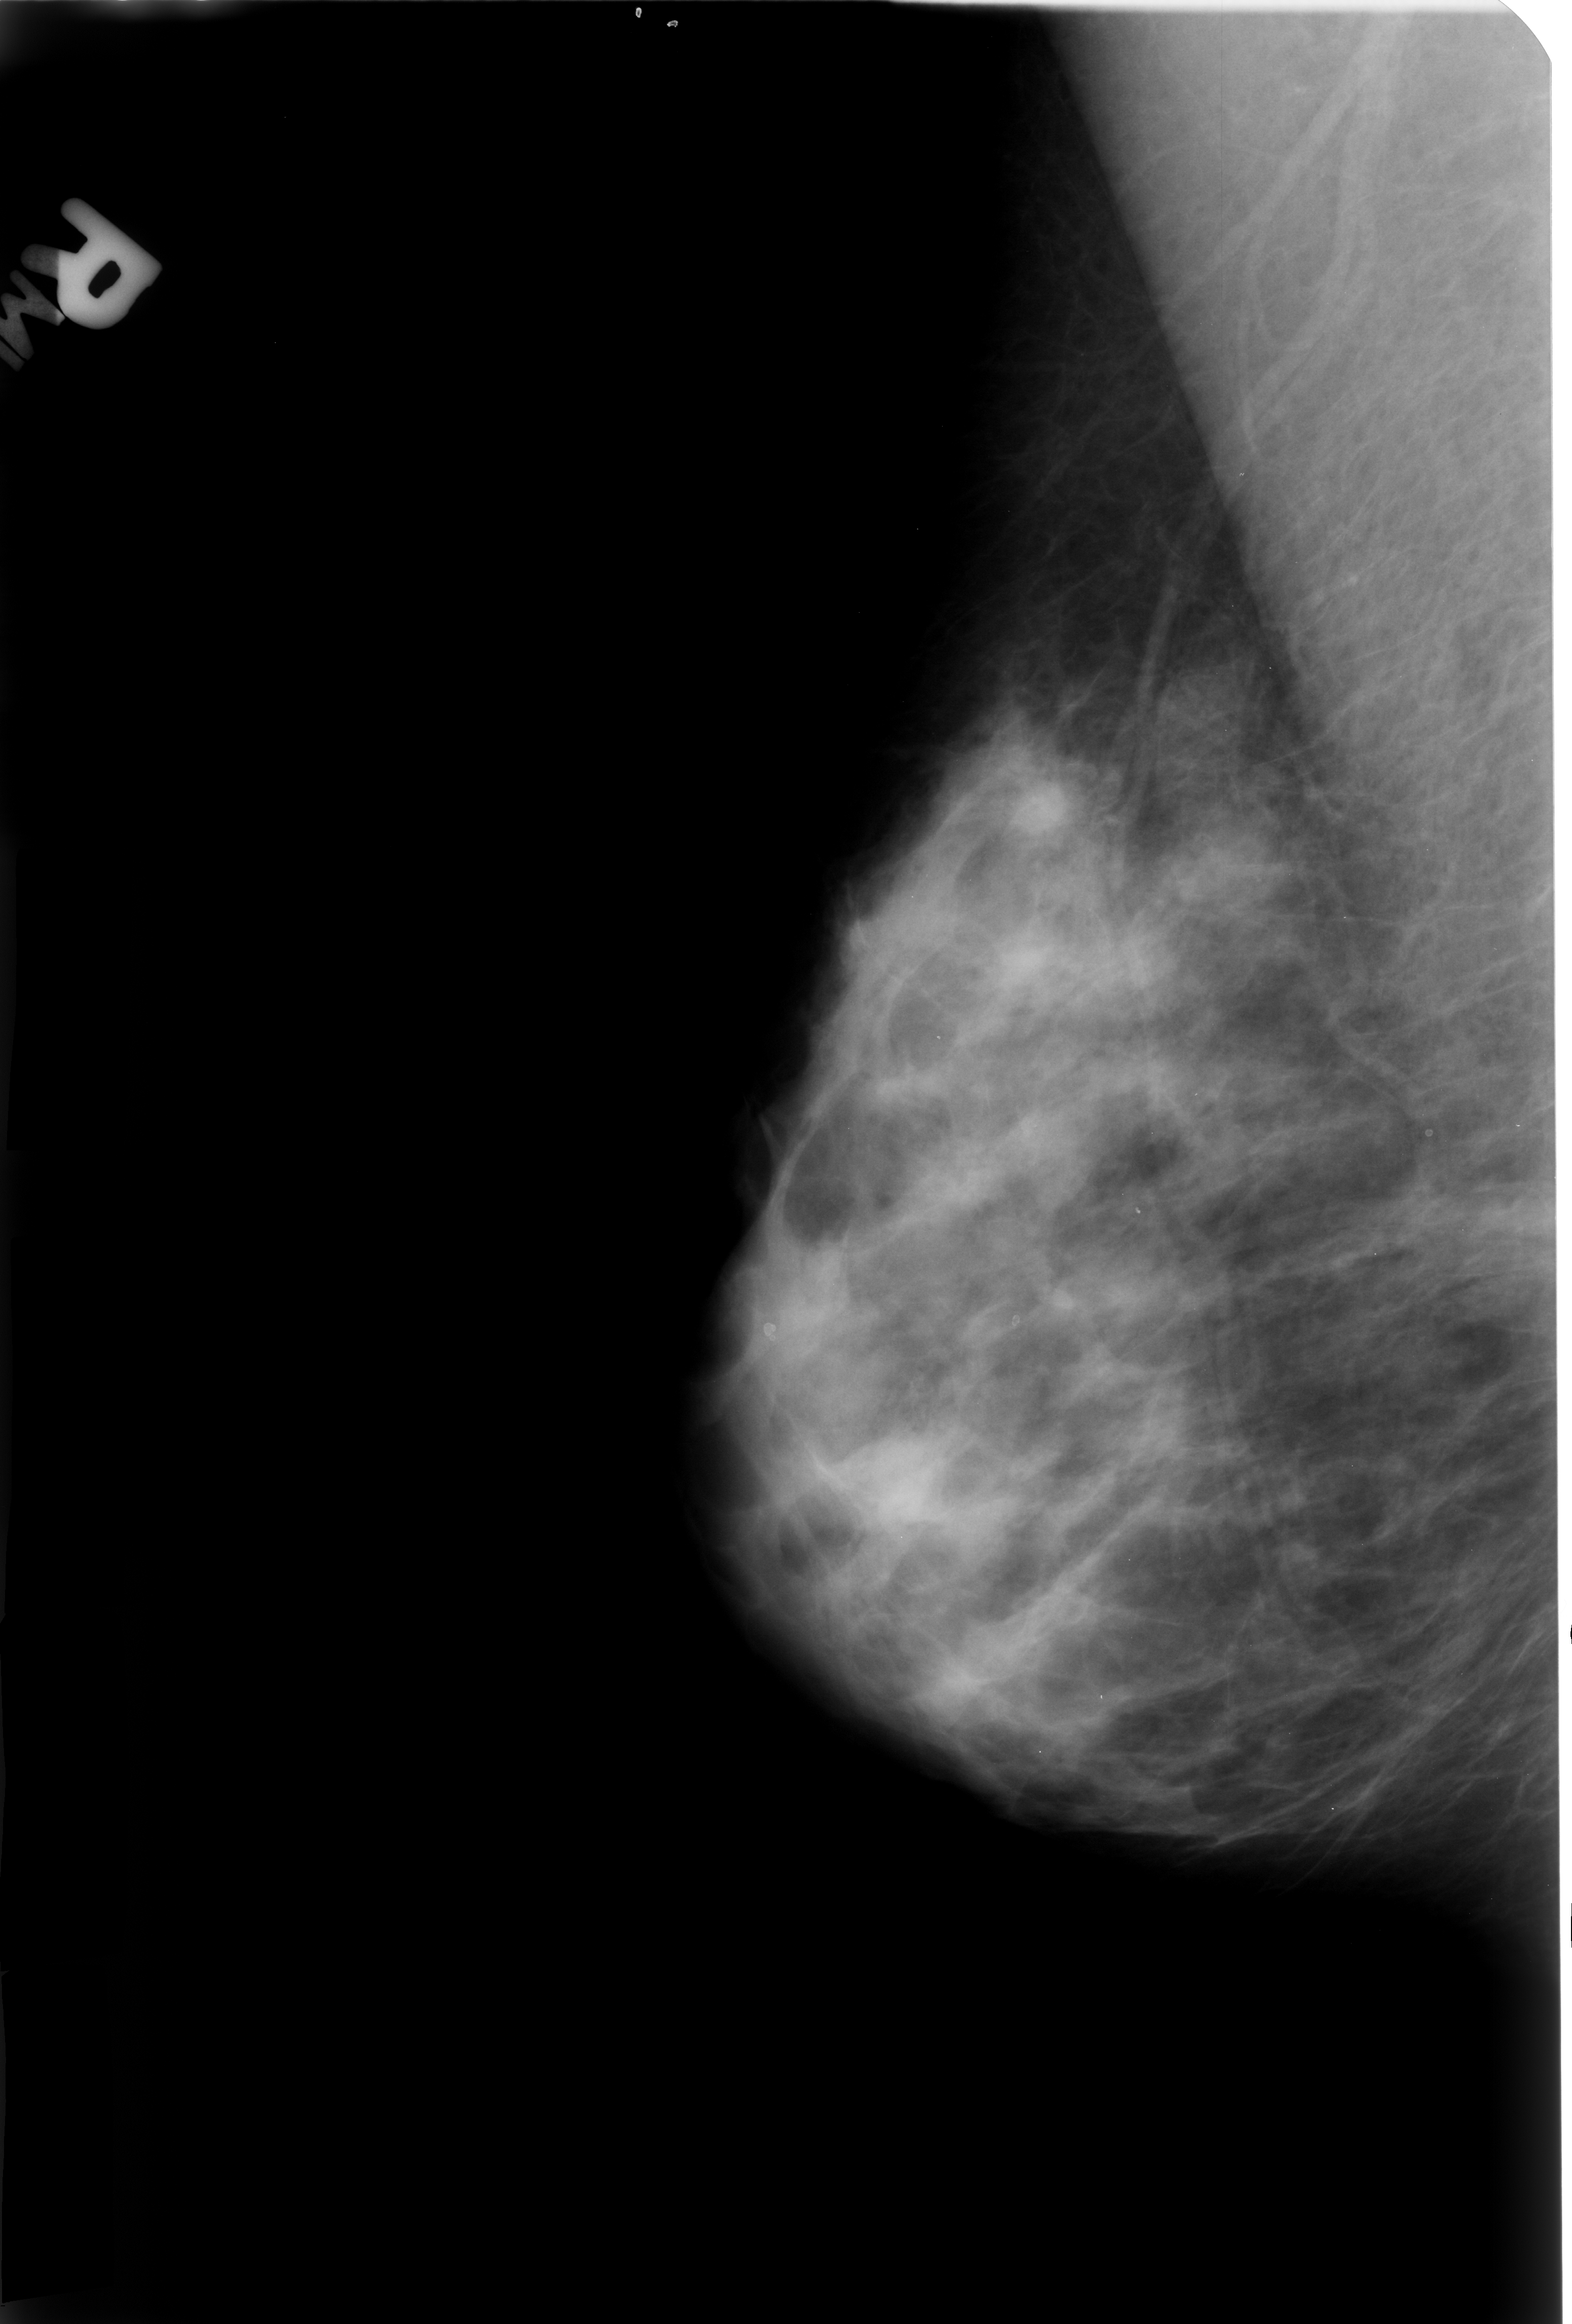
Digitized screen-film mammogram; right breast; mediolateral oblique (MLO) view; BI-RADS breast density category 3 (scale 1–4).
- Calcifications, morphology lucent center; BI-RADS assessment category 2; benign without callback (not worked up further).